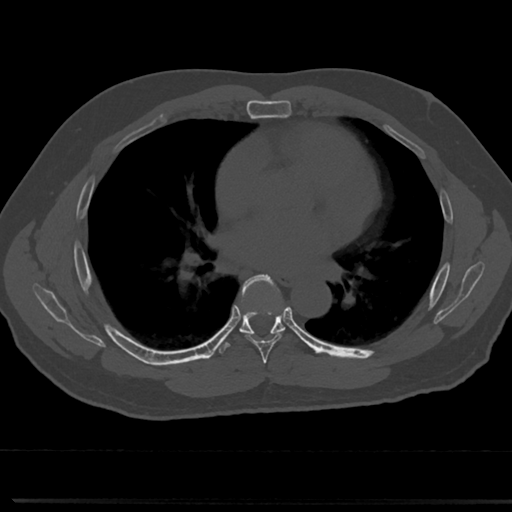
CT including the spine, one axial slice; reconstruction kernel Br40s/3; bone window (W 1800 / L 400 HU); 0.5 mm slice thickness; 512 × 512 image matrix, field of view 355 × 355 mm. Male patient, age 61 years. From the clinical record (not read from this slice): primary cancer: prostate.
Outlined on this slice (semi-automatically segmented with operator editing):
- T5 vertebra: bounding box <265,370,271,376> (left, top, right, bottom; pixels)
- T6 vertebra: <238,276,289,357>
- T7 vertebra: <241,326,284,334>